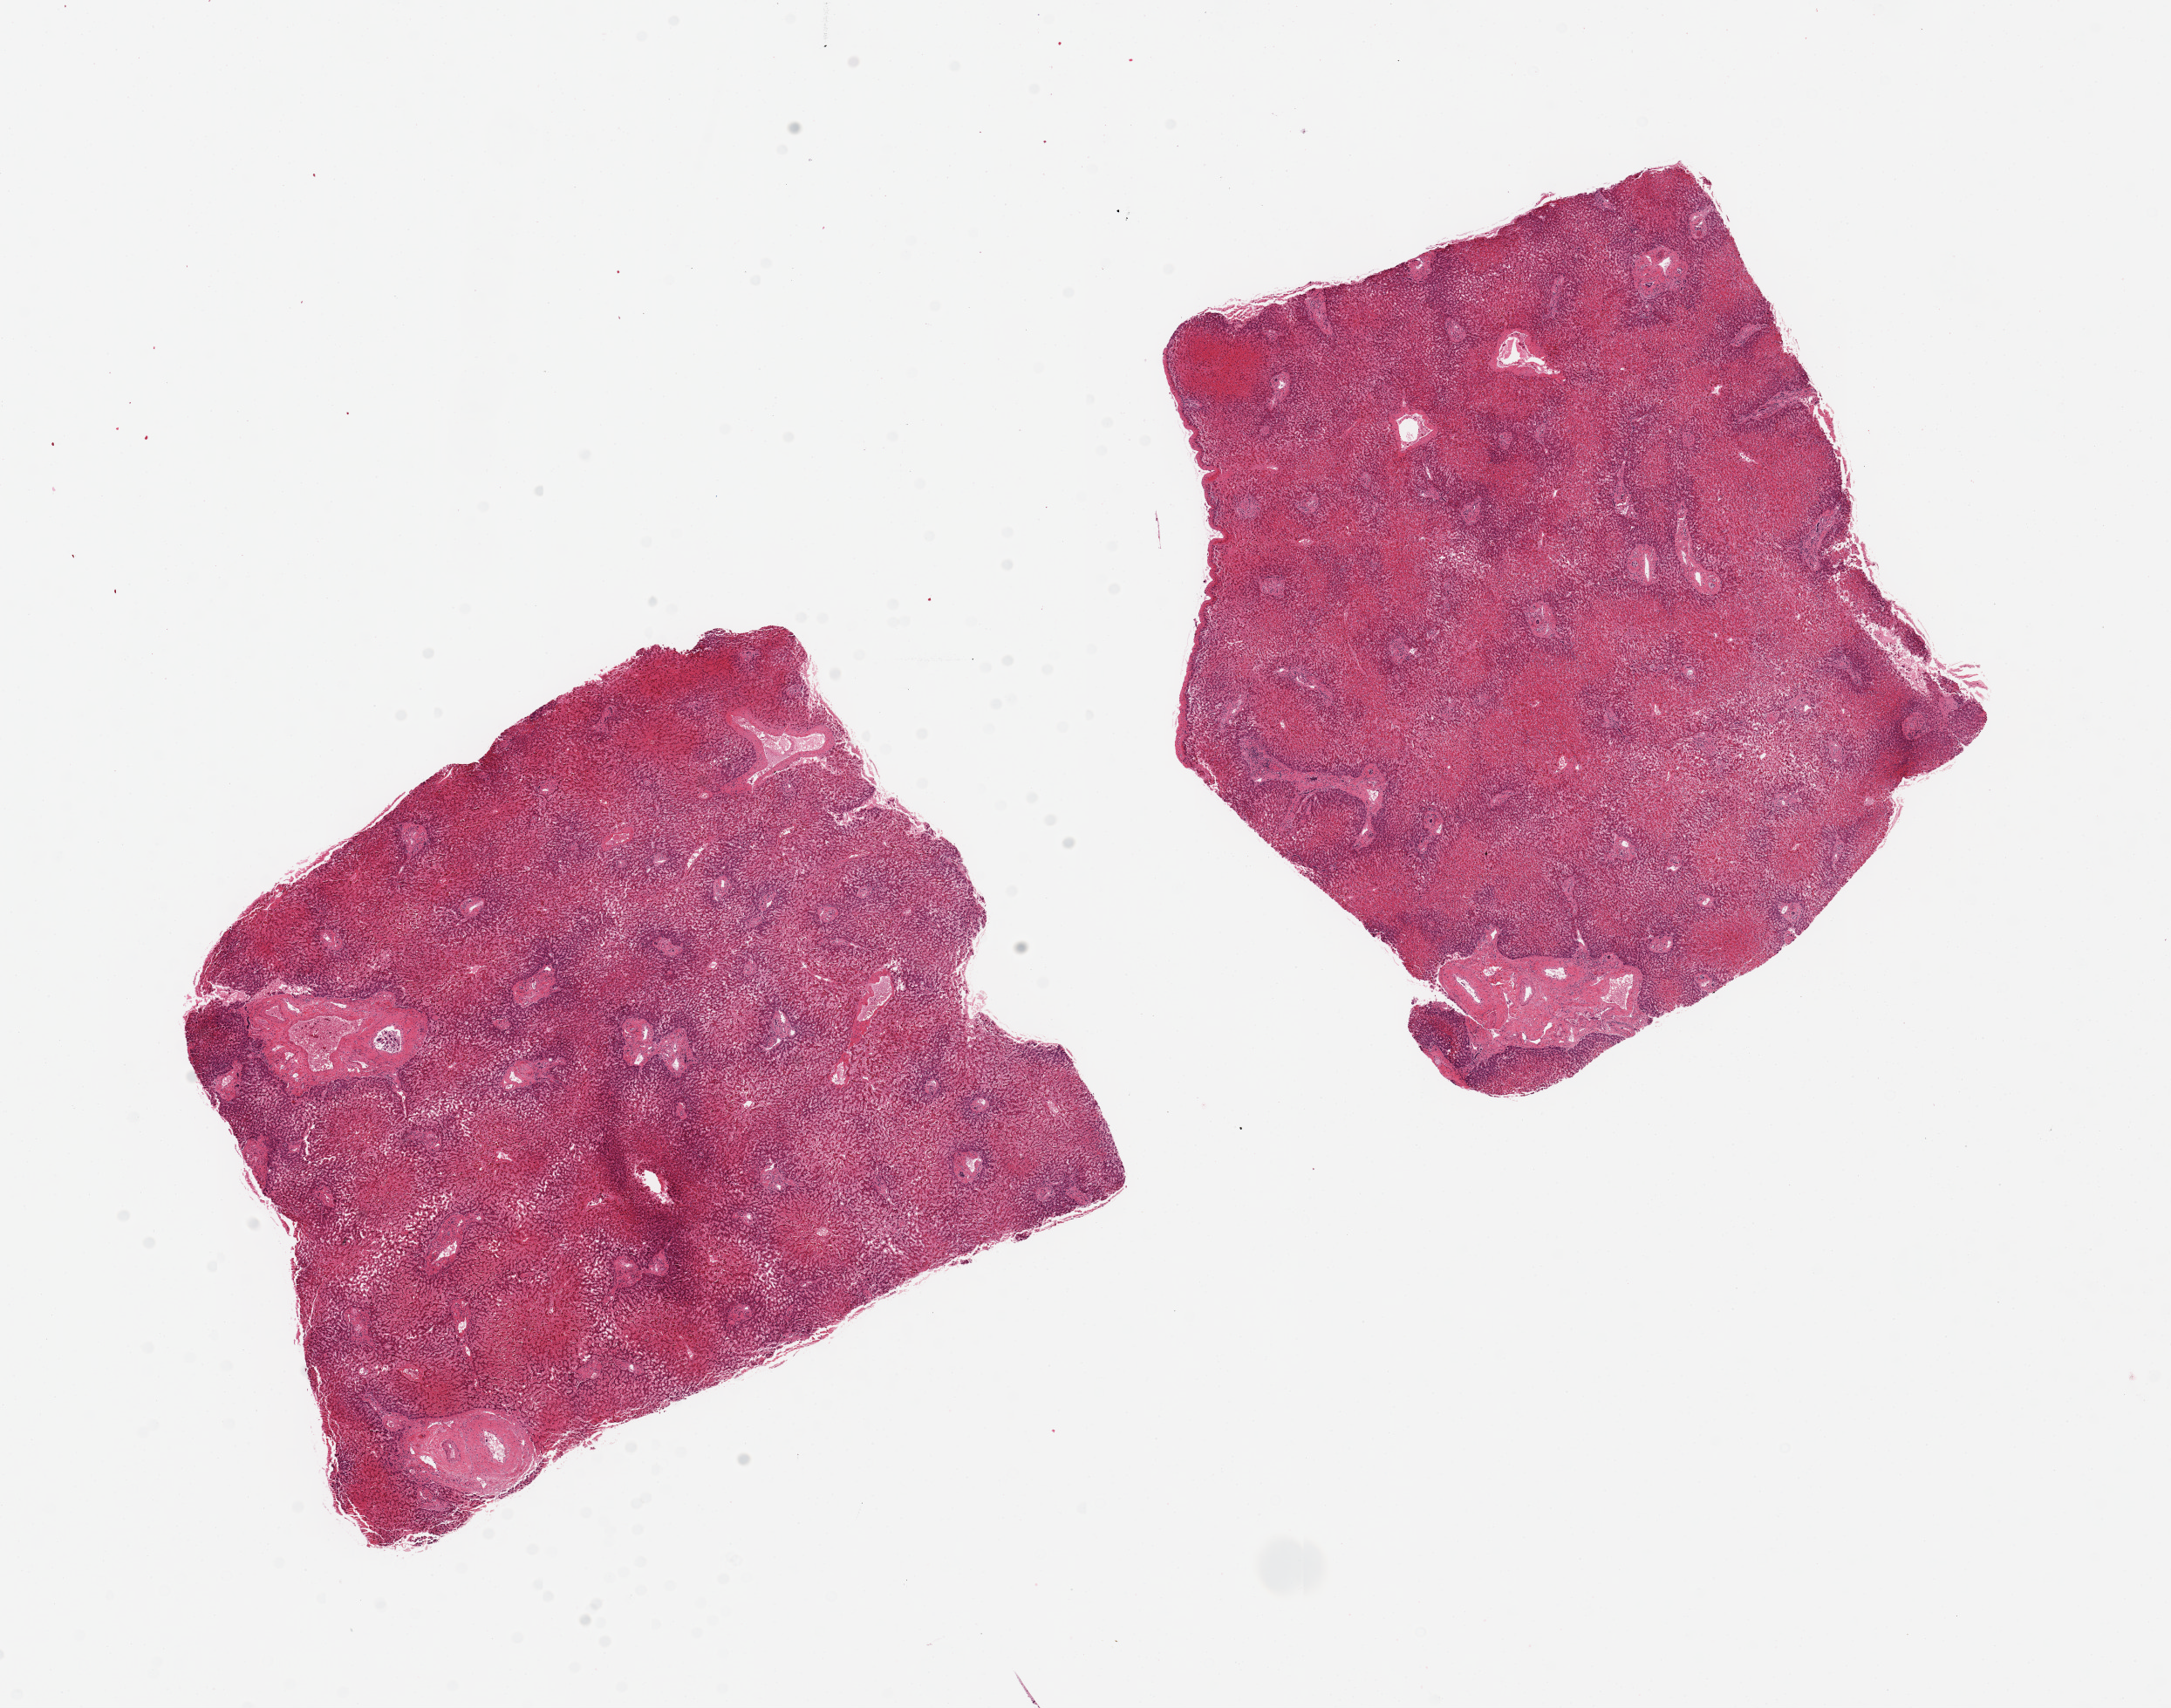
Whole-slide image, H&E stain, low-resolution overview of the scanned area, about 19.7 x 15.5 mm (slide scanned at 20x), PAXgene-fixed paraffin-embedded (PFPE) section, target tissue: liver, tissue donor sample. Donor sex: female.
- reviewer comment on this tissue sample: 2 pieces, 8x6 & 8x7mm; Moderate to severe central congestion